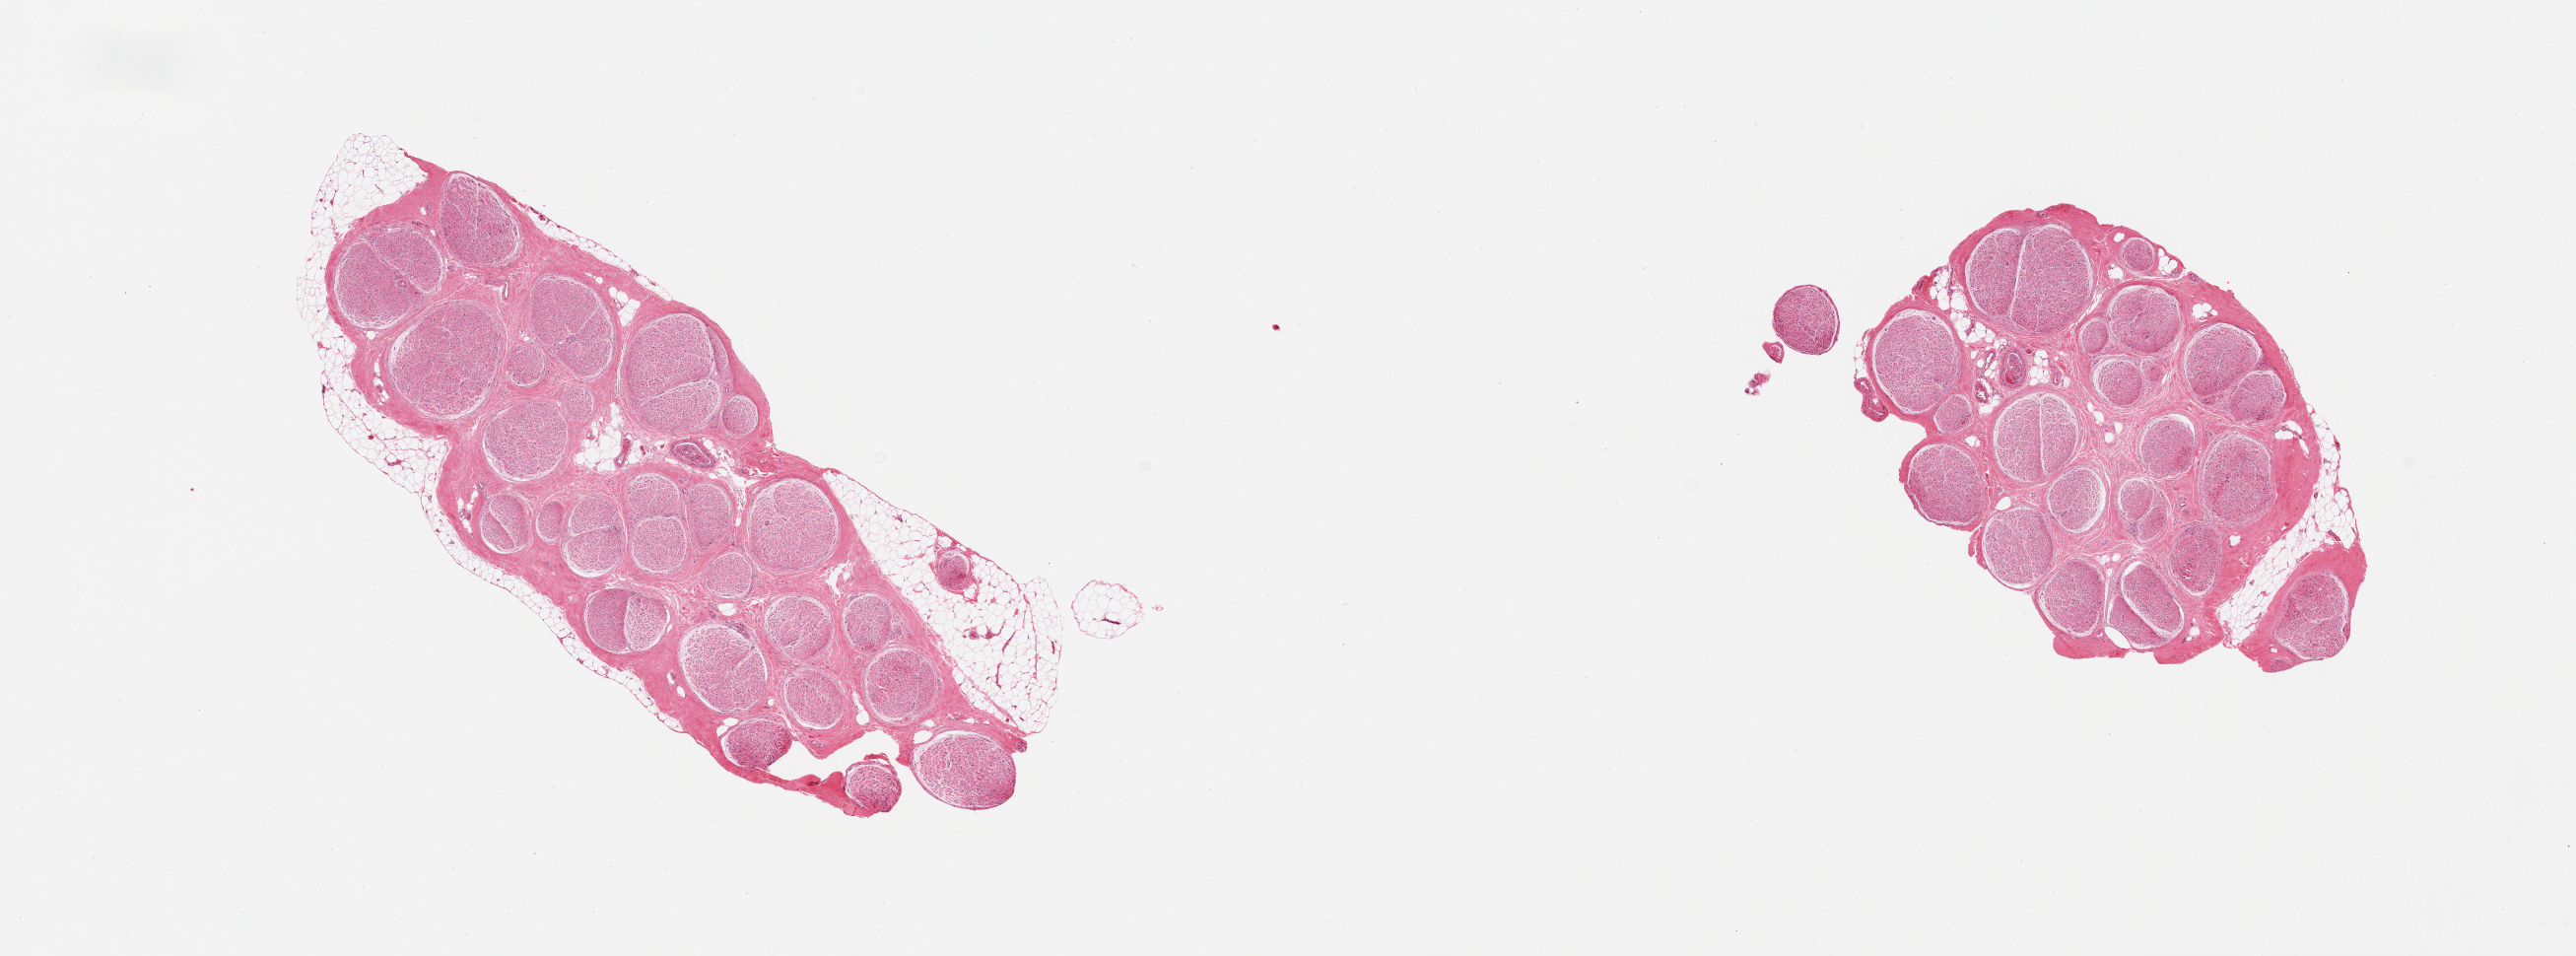
Hematoxylin and eosin (H&E) whole-slide image, brightfield — whole scanned area (about 20.7 x 7.7 mm, from a 20x scan) shown as a low-resolution overview, PAXgene-fixed, paraffin-embedded tissue, sampled site (target tissue): tibial nerve, donor tissue sample. Male donor.
• pathologist's review note for this sample: 2 pieces, 5-15% attached fat